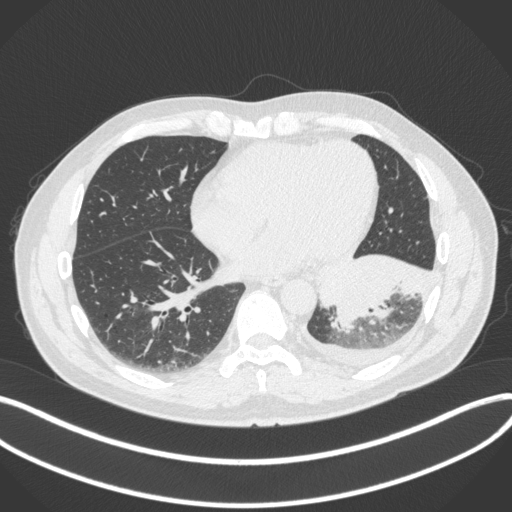
Chest CT, one axial slice; position 128 of 350 along the scan axis; reconstruction kernel B31f; lung window (W 1500 / L -600 HU); 1 mm slice thickness; 512 × 512 image matrix, field of view 400 × 400 mm. Male patient, age 58 years. From the clinical record (not read from this slice): clinical TNM (as recorded): T3 N1 M1b; histopathological grade: G3.
Annotated regions visible in this slice (rectangle marked by the reading radiologist):
- lung tumour (recorded histology: small cell carcinoma): bounding box <315,248,434,339> (left, top, right, bottom; pixels)